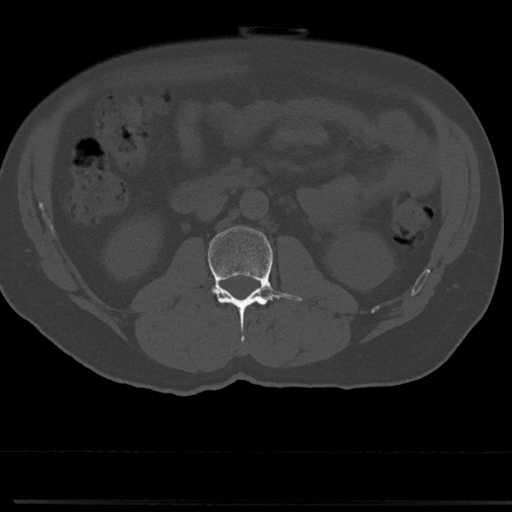
CT including the spine, one axial slice. Slice 11 of 817 in the series (ordered by position). 120 kVp. Bone window (W 1800 / L 400 HU). 512 × 512 image matrix. Male patient, age 61 years. Case-level facts recorded for this patient, not image findings: primary cancer: prostate.
Structures marked on this image (semi-automatic segmentation, software-assisted and operator-edited):
- L2 vertebra: bounding box [x1, y1, x2, y2] px = [208, 226, 303, 343]